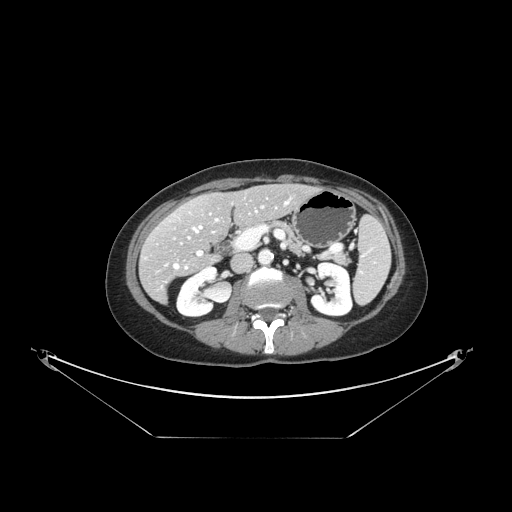
Contrast-enhanced abdominal CT, one axial slice; slice 69 of 148 in the series (ordered by position); reconstruction kernel STANDARD; 120 kVp; intravenous contrast given; soft-tissue window (W 400 / L 40 HU); 512 × 512 image matrix. Female patient, age 73 years. Case-level facts recorded for this patient, not image findings: diagnosis: colorectal cancer liver metastases, imaged before liver resection; multiple liver metastases: no; largest metastasis: 1 cm; disease in both lobes: no.
Structures marked on this image (outlined manually by an expert reader):
- hepatic veins: bounding box [x1, y1, x2, y2] px = [174, 201, 289, 269]
- liver: [141, 185, 314, 301]
- planned liver remnant (the part of the liver to remain after resection): [167, 186, 314, 248]
- portal vein (with intrahepatic branches): [197, 251, 202, 256]